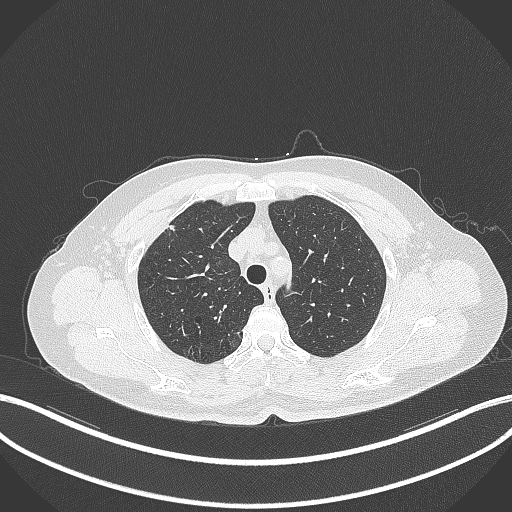
Chest CT, one axial slice. Slice 290 of 353 in the series (ordered by position). Reconstruction kernel B70f. 120 kVp. Lung window (W 1500 / L -600 HU). 1 mm slice thickness. 512 × 512 image matrix. Patient: female, 56 years. From the clinical record (not read from this slice): clinical TNM (as recorded): T1c N0 M0.
Outlined on this slice (bounding box drawn by a radiologist):
- lung tumour (recorded histology: adenocarcinoma): bounding box (x1, y1, x2, y2) in pixels: (159, 217, 181, 233)